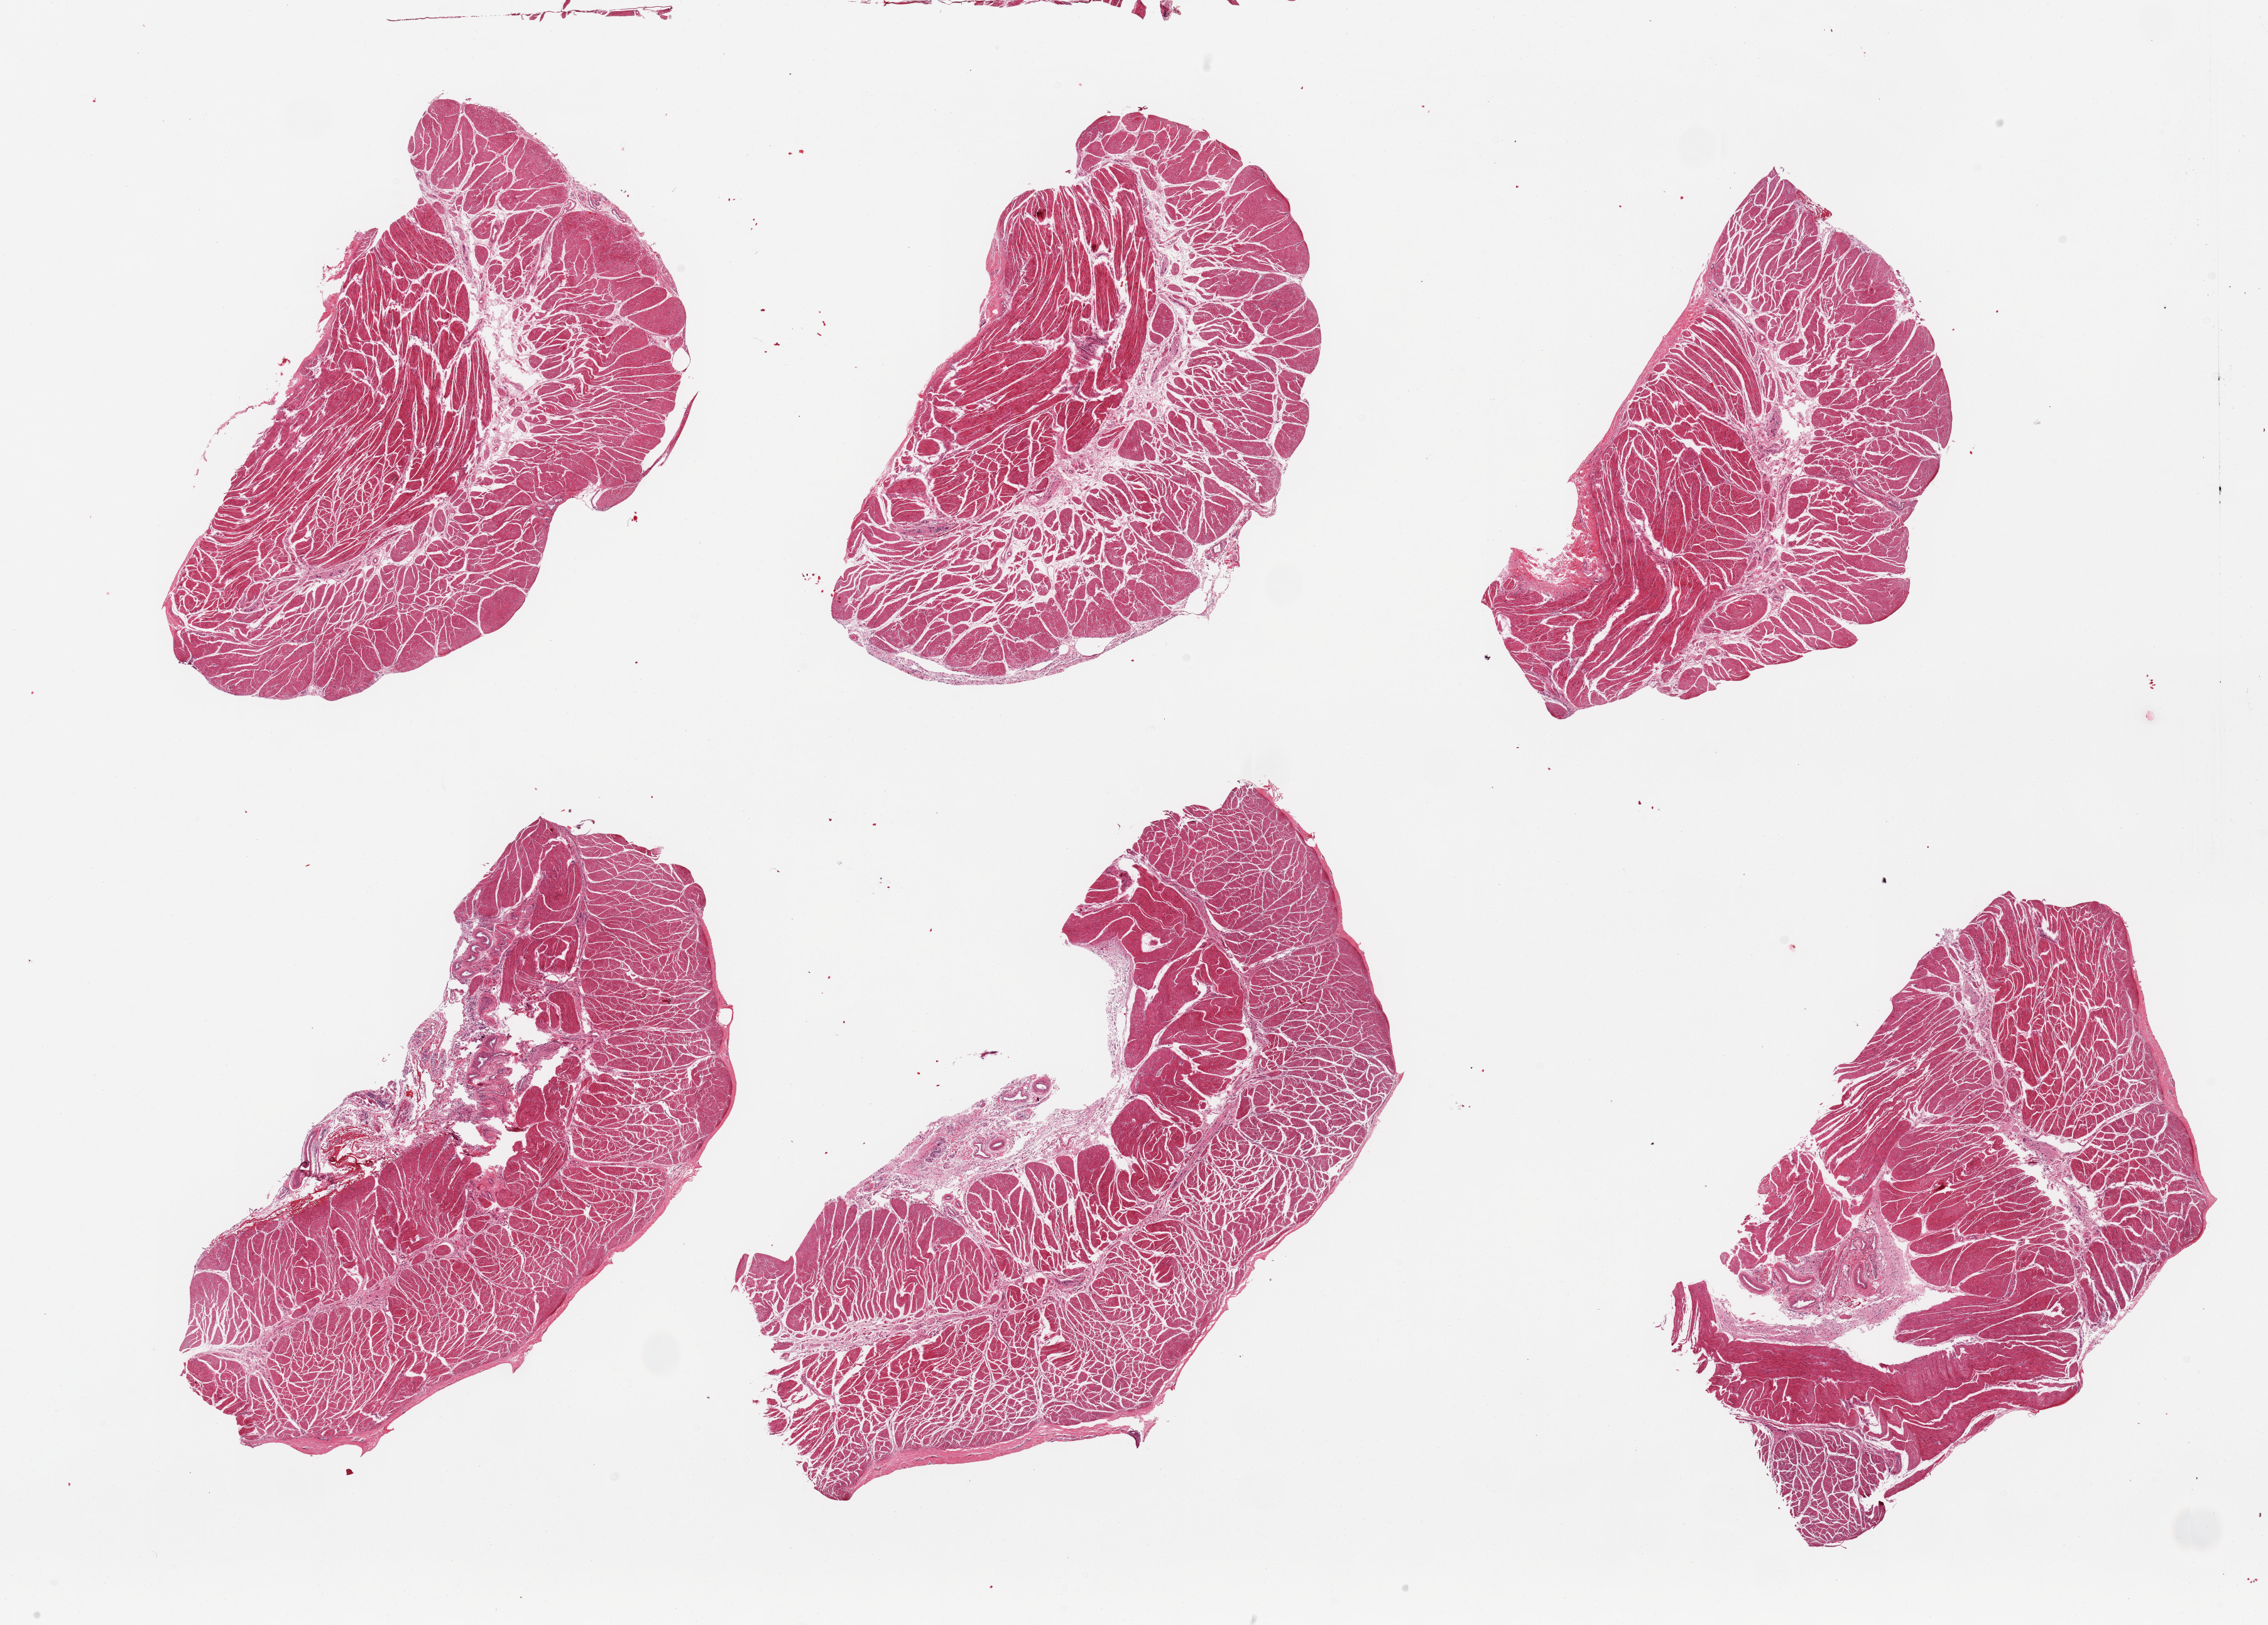
Digitized H&E-stained section, shown as a low-resolution overview of the whole scanned area (about 28.5 x 20.5 mm), PAXgene-fixed, paraffin-embedded tissue, target tissue: esophageal muscle, tissue donor sample. Female donor.
Pathologist's review note for this sample: 6 pieces; well trimmed.